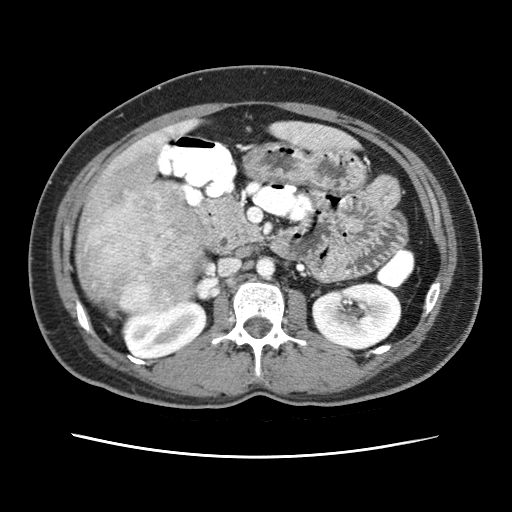
Contrast-enhanced abdominal CT (liver protocol), one axial slice. Slice 14 of 79 in the series (ordered by position). Reconstruction kernel STANDARD. 120 kVp. Soft-tissue window (W 400 / L 40 HU). 2.5 mm slice thickness. 512 × 512 image matrix, field of view 340 × 340 mm. From the clinical record (not read from this slice): diagnosis: hepatocellular carcinoma (patient treated with transarterial chemoembolisation; whether this scan precedes or follows treatment is not stated here); TNM stage (as recorded): Stage-I; Child-Pugh class: A; tumour differentiation: moderately differentiated; tumour nodularity: uninodular.
Outlined on this slice (semi-automatically segmented with operator editing):
- abdominal aorta: bounding box [x1, y1, x2, y2] px = [256, 256, 275, 276]
- liver parenchyma outside the tumour (the mass and vessels are separate outlines, so this box may not span the whole liver): [76, 128, 238, 302]
- mass: [76, 155, 207, 316]